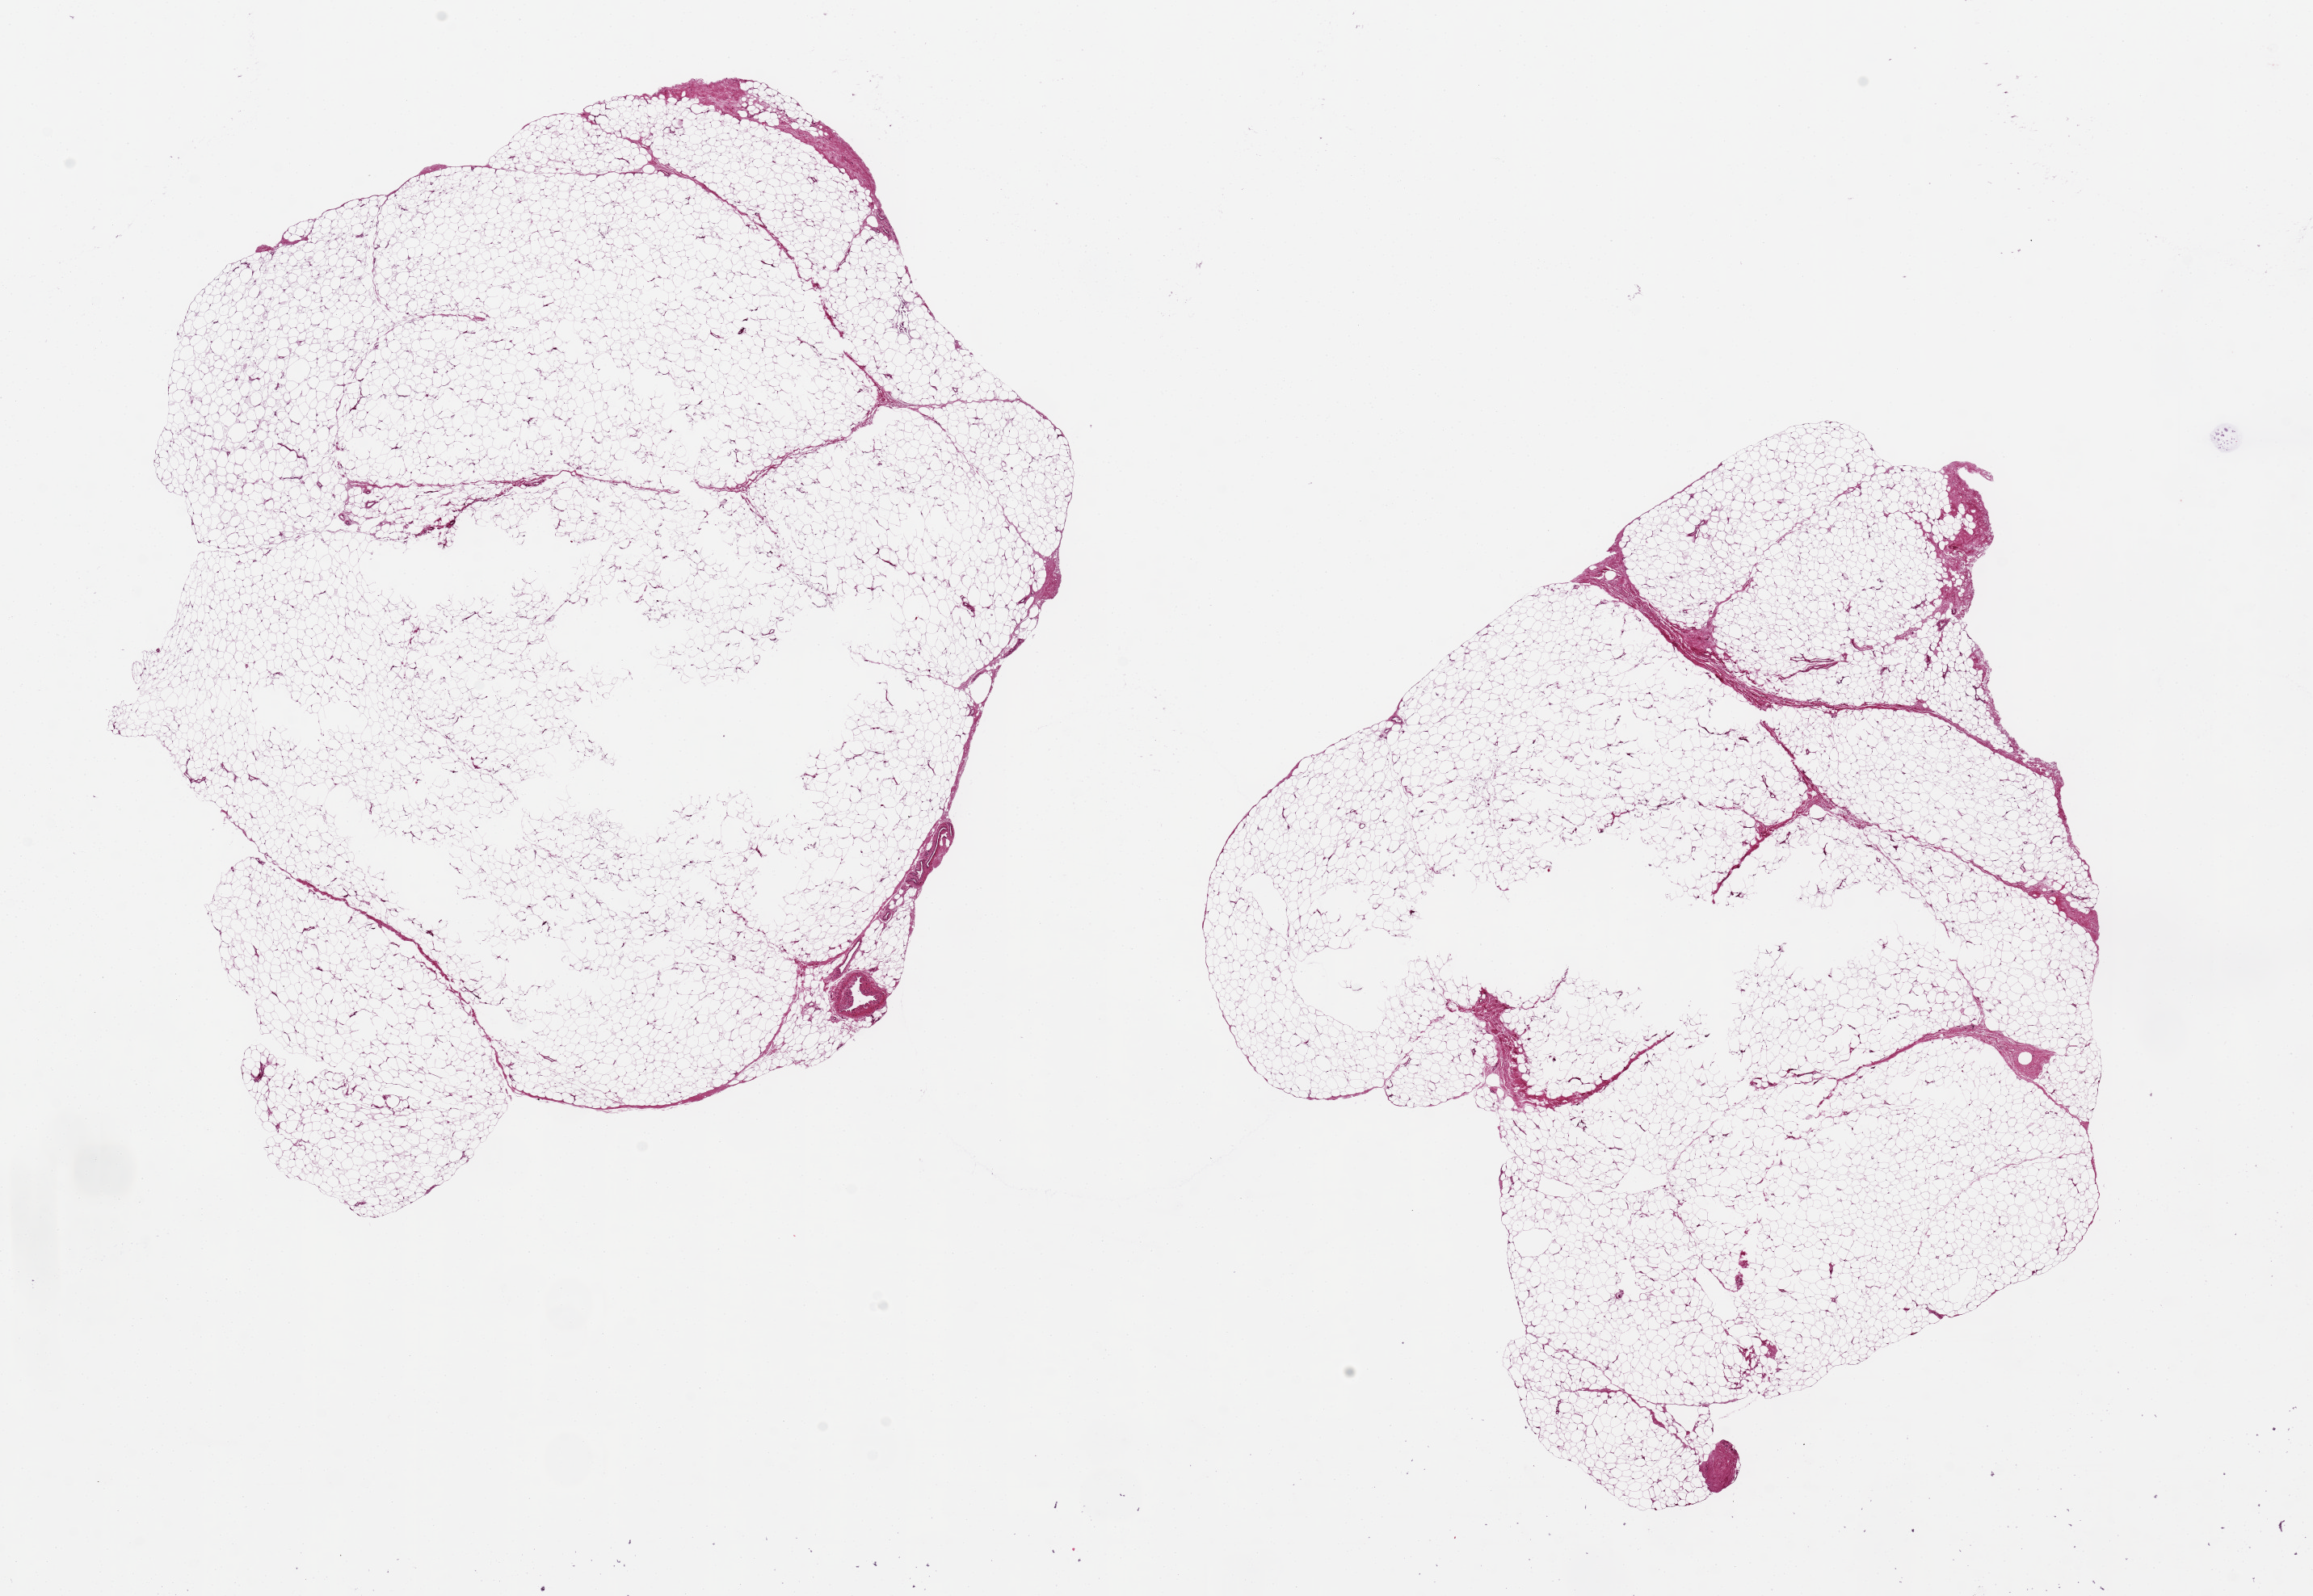
Digitized H&E-stained section, brightfield, low-resolution overview of the scanned area, about 22.6 x 15.6 mm; PAXgene-fixed paraffin-embedded (PFPE) section; section of adipose tissue (target tissue); tissue donor sample. Donor sex: male.
• pathologist's review note for this sample: 2 aliquots, ~10x8mm